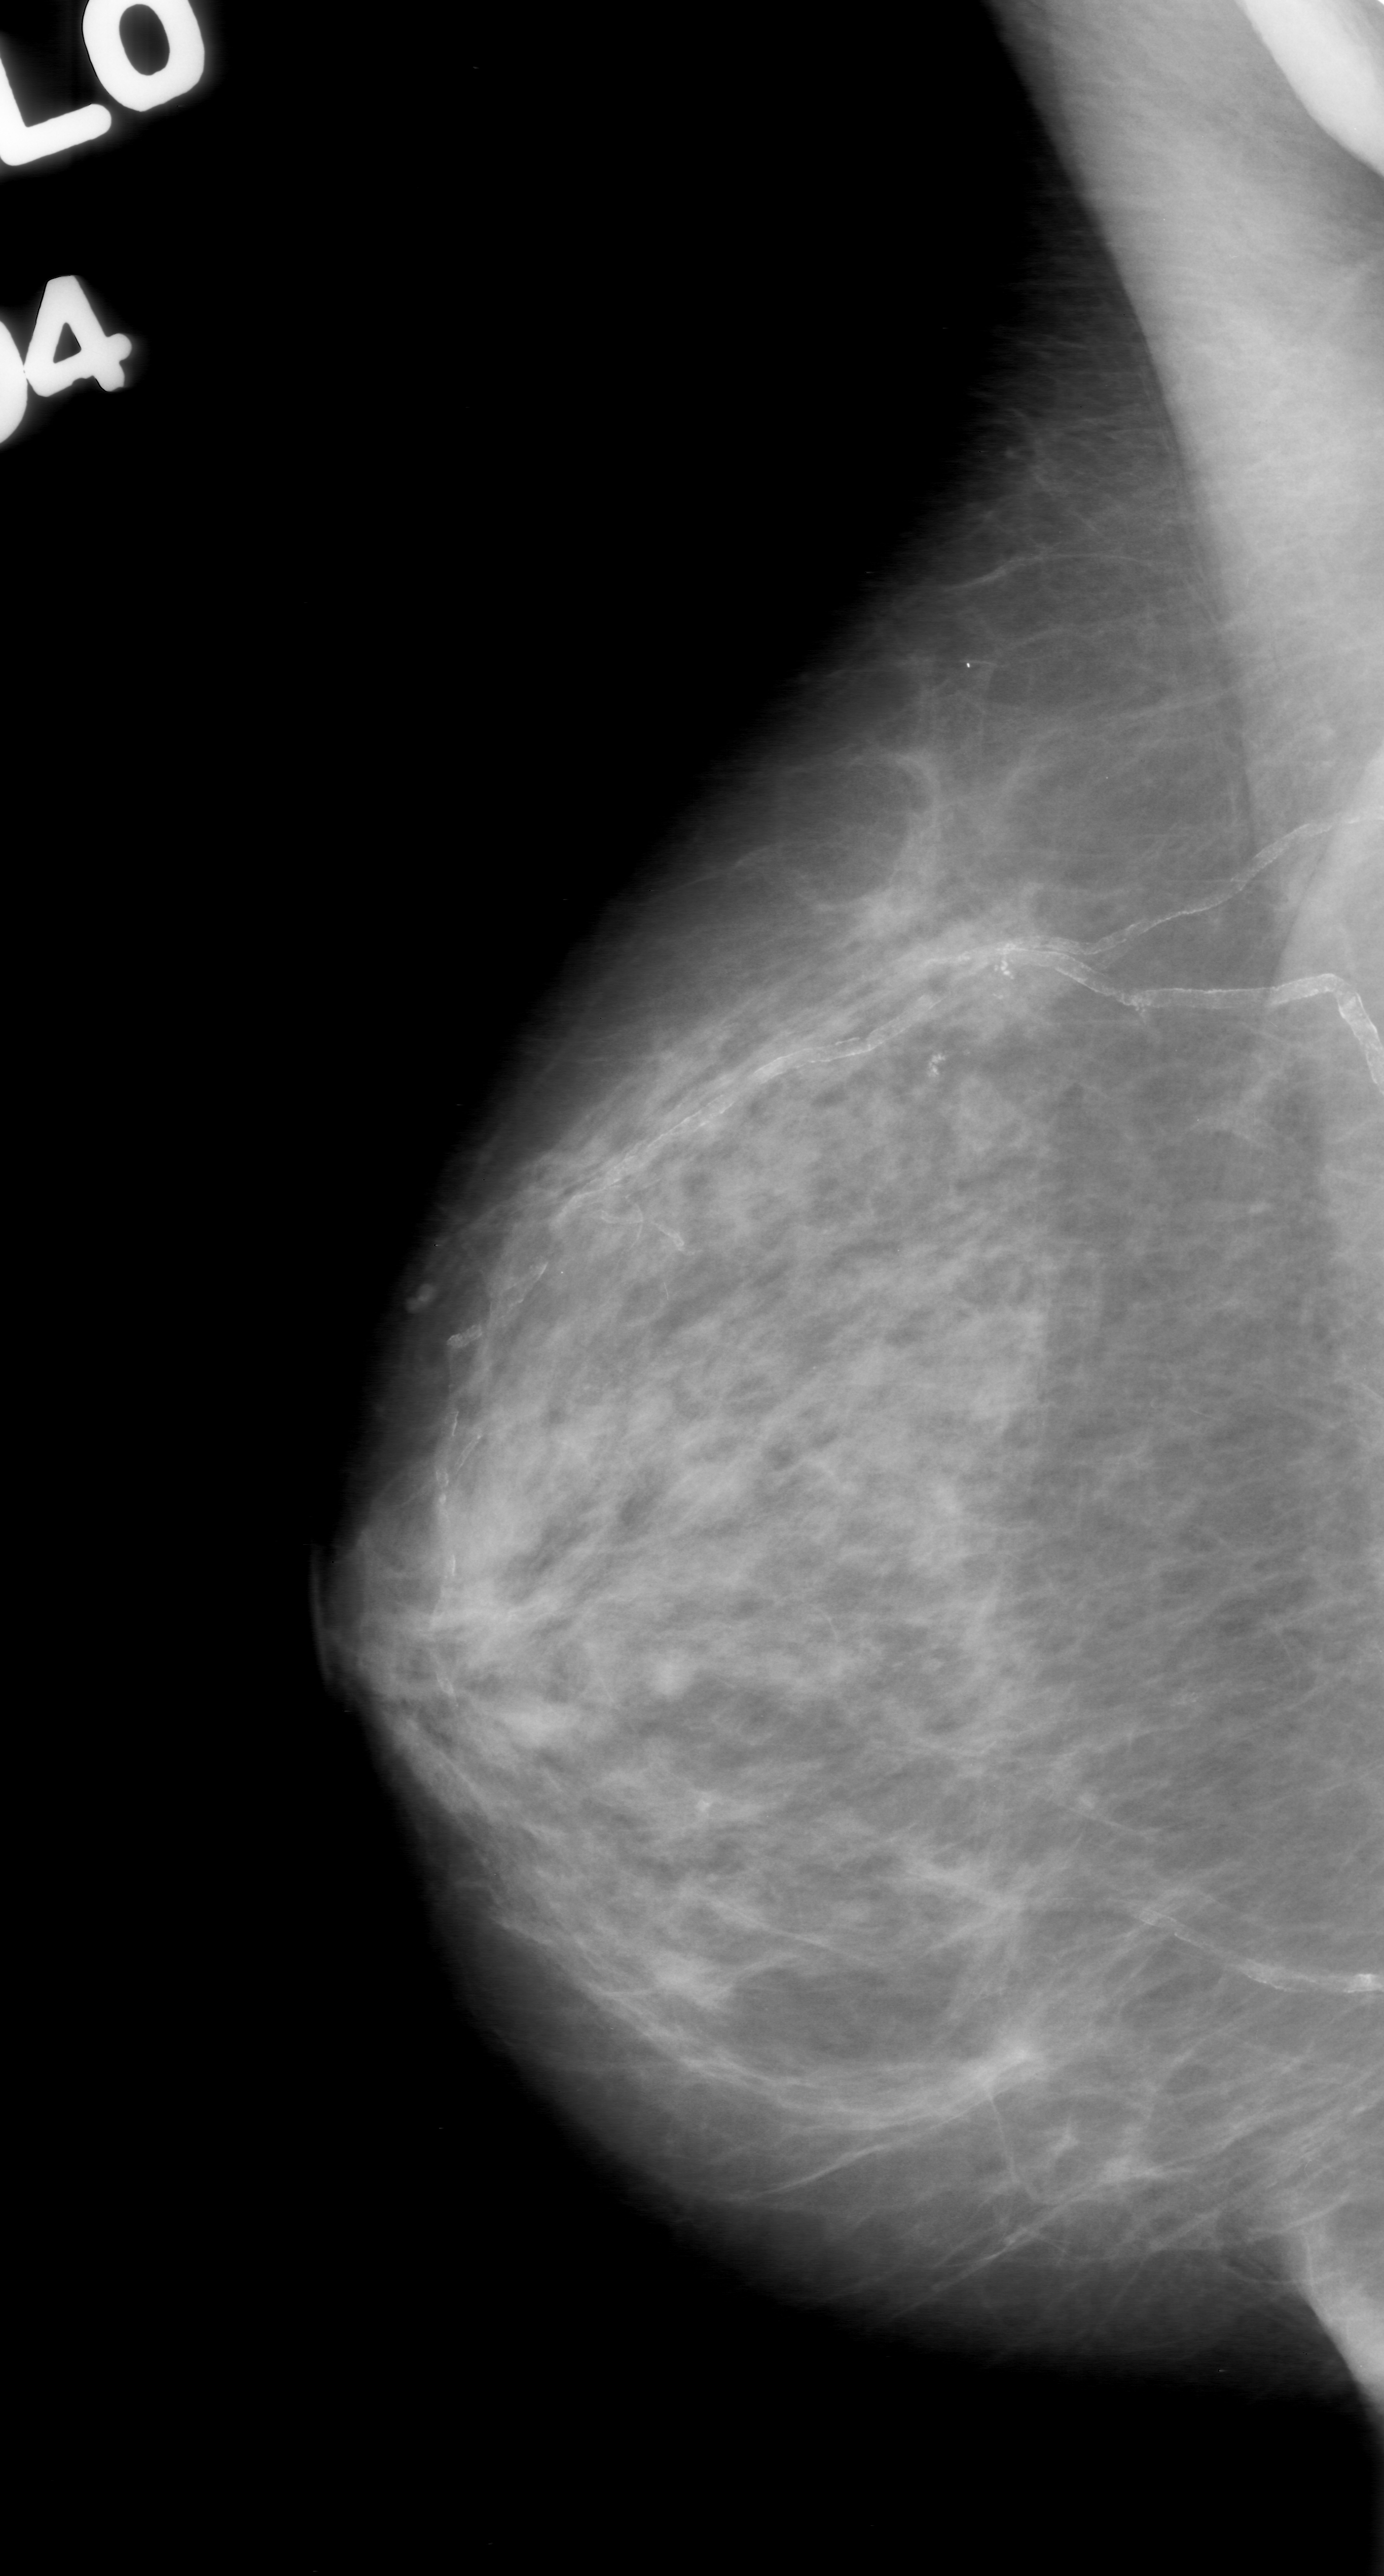
Digitized screen-film mammogram, right breast, MLO view, BI-RADS breast density category 3 (scale 1–4).
- Calcifications, morphology coarse, distribution clustered; BI-RADS assessment category 0 (incomplete: needs additional imaging); subtlety rating 5 on a 1 (subtle) to 5 (obvious) scale; pathology result (as recorded, not read from the image): benign.